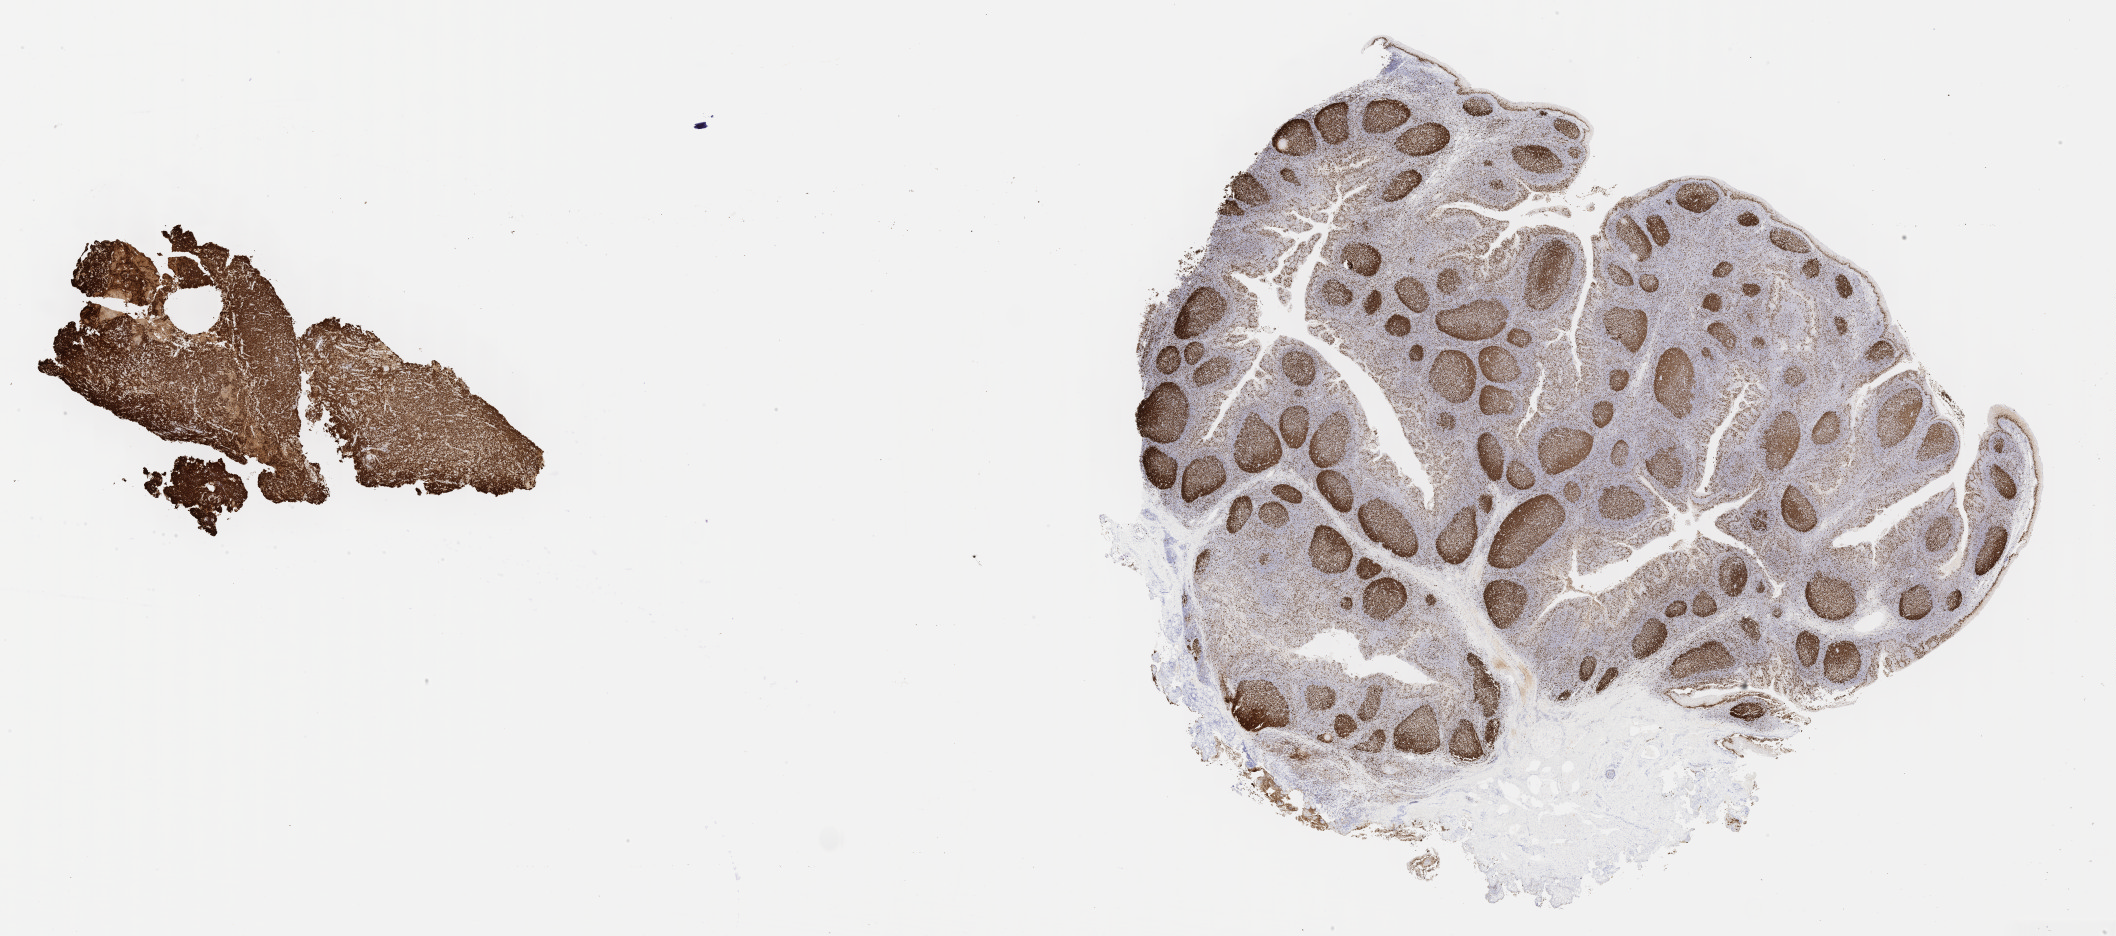
Immunohistochemistry (IHC) whole-slide image stained for Ki-67, shown as a low-resolution overview of the whole scanned area (about 34.2 x 15.1 mm); tumor tissue; site: mandible. Male patient, 25 years old.
Diagnosis: Diffuse large B-cell lymphoma, NOS.